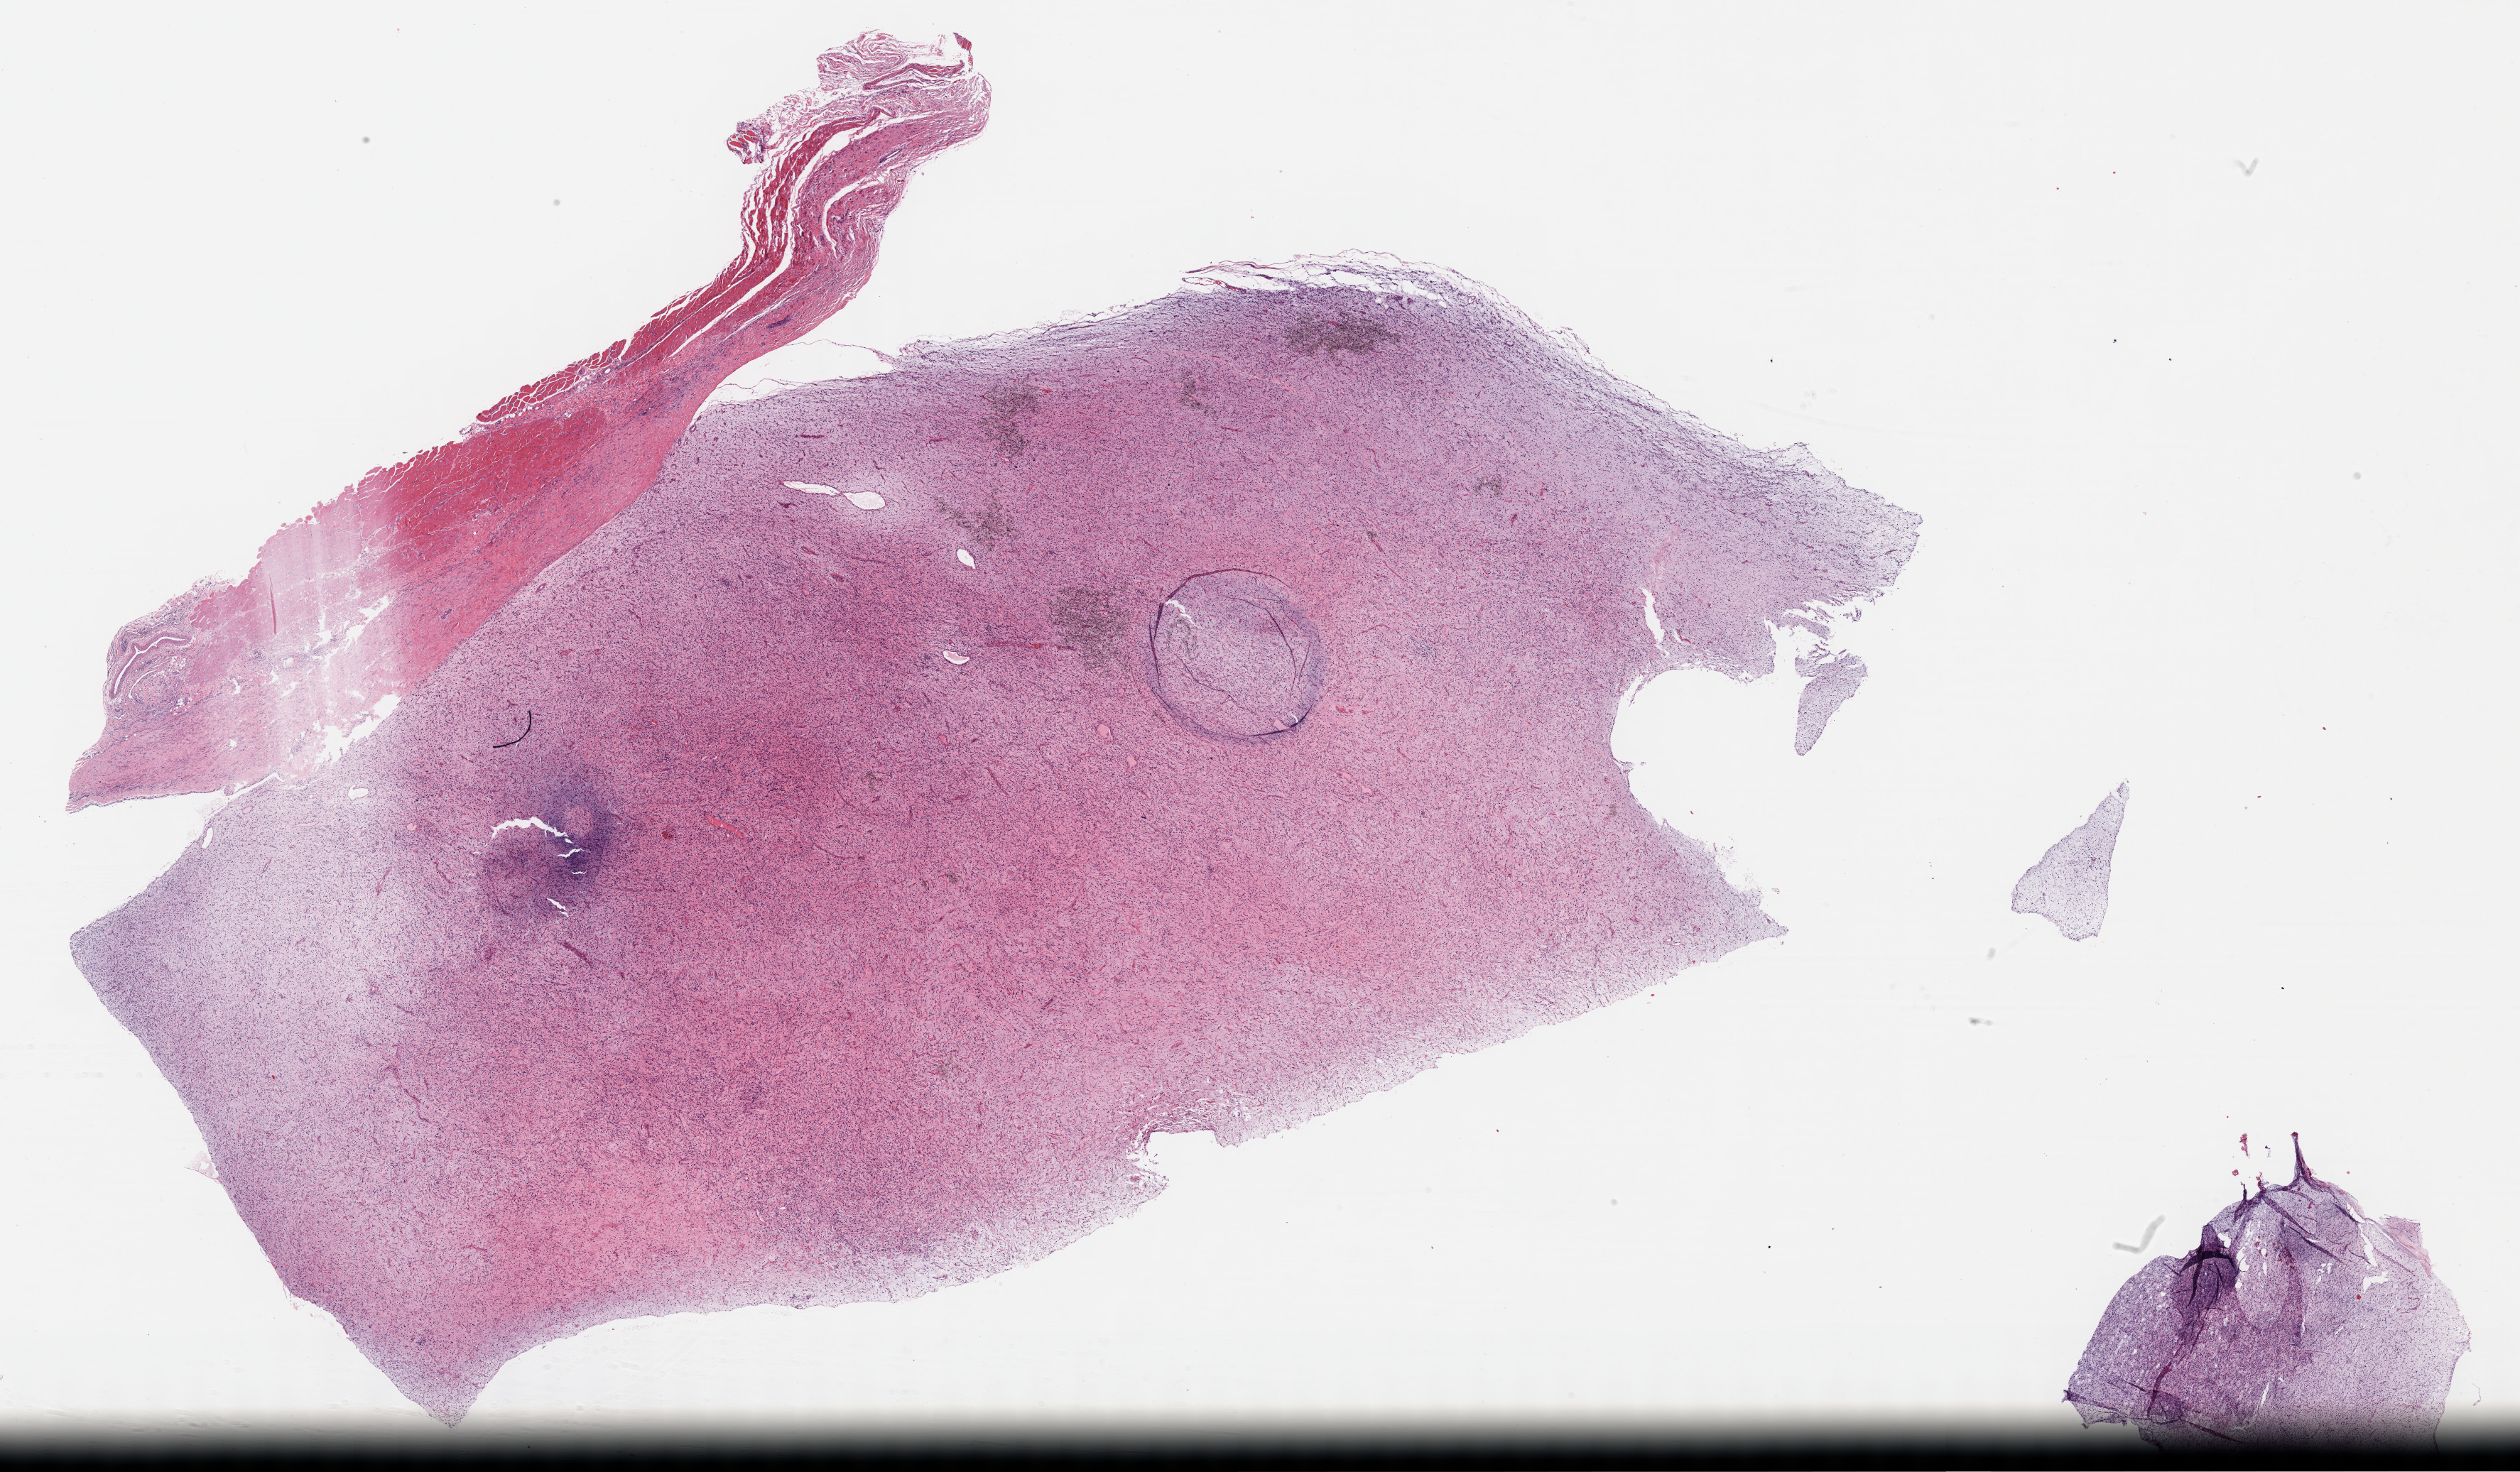
Digitized H&E-stained tissue section (whole slide) — low-resolution overview of the scanned area, about 28.7 x 16.8 mm (acquisition: 40x scan); FFPE section; sample: primary tumour, connective, subcutaneous and other soft tissues. Male, age 35 years at initial diagnosis.
Histologic diagnosis: Fibromyxosarcoma (connective, subcutaneous and other soft tissues of lower limb and hip).